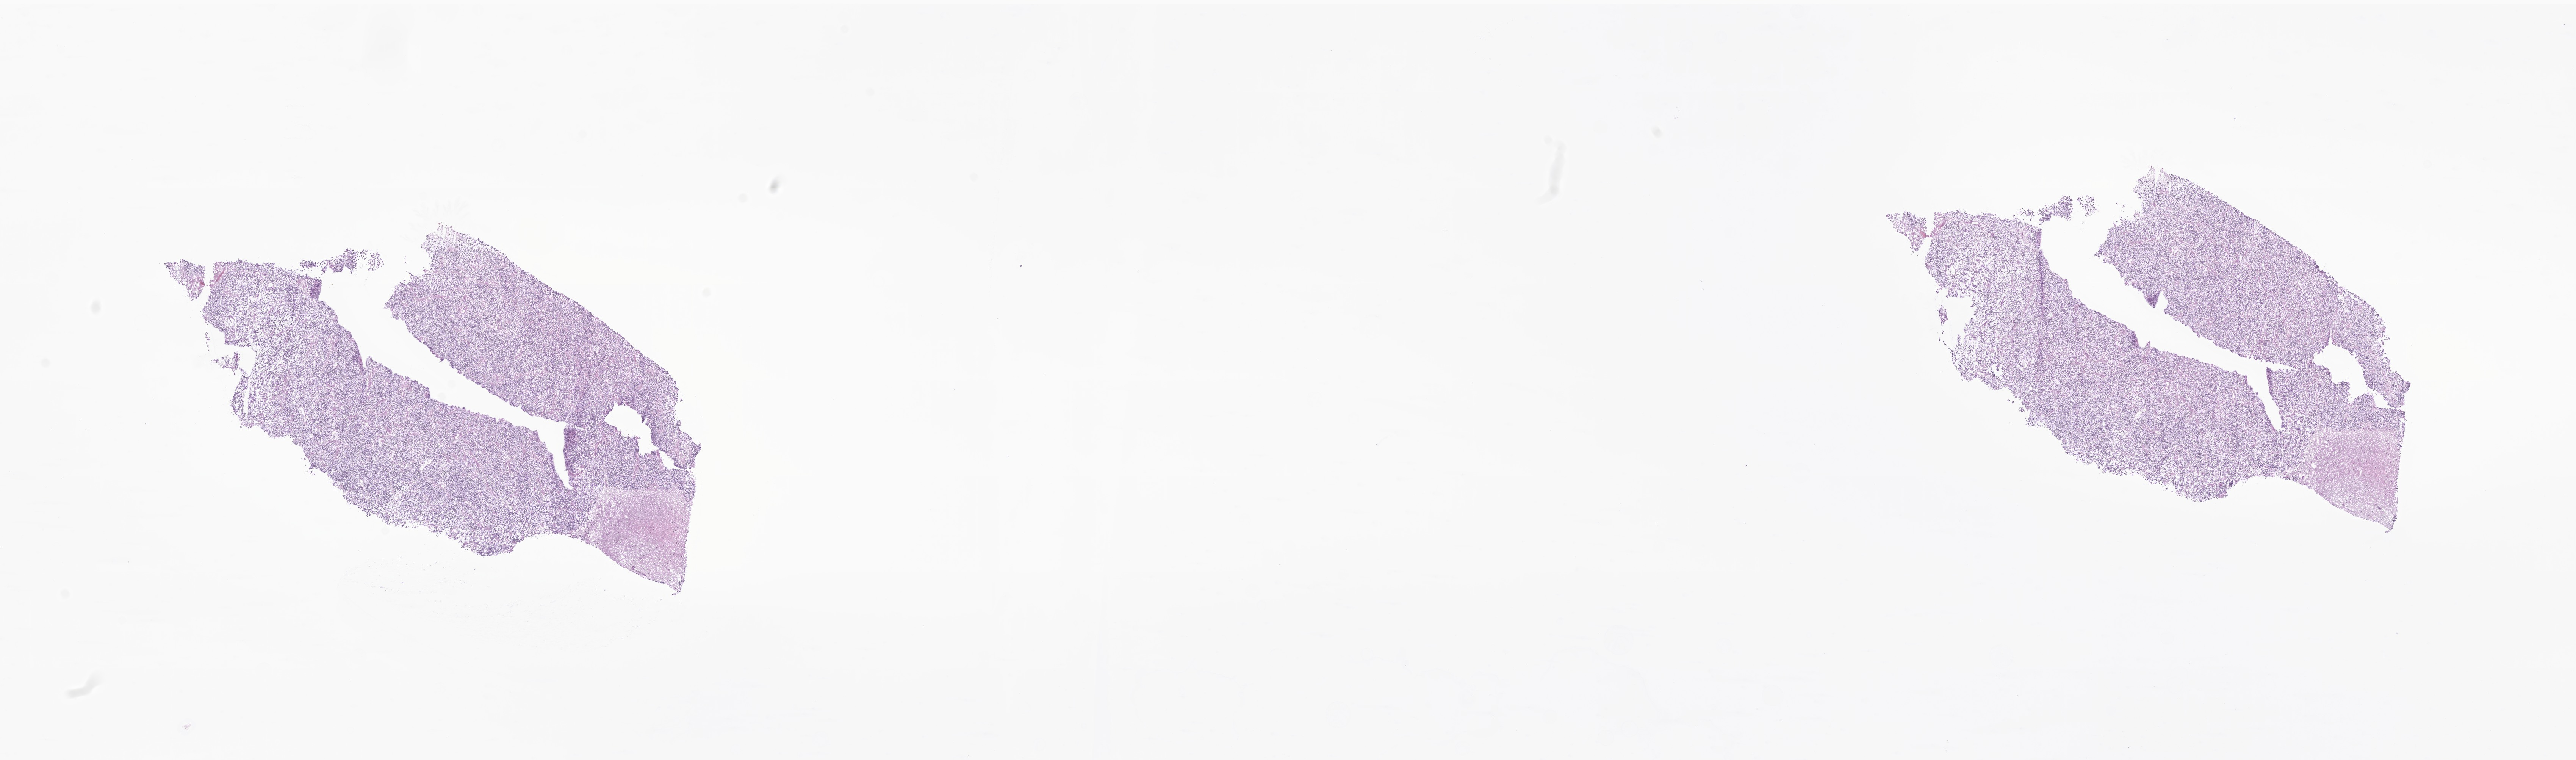
Haematoxylin and eosin whole-slide image of tumor tissue from the parietal lobe — shown as a low-resolution overview of the whole scanned area (about 28.7 x 8.5 mm), cryosection (OCT / tissue freezing medium). Female patient, age 126 months (10 years 6 months).
Recorded diagnosis: Neoplasm, uncertain whether benign or malignant.